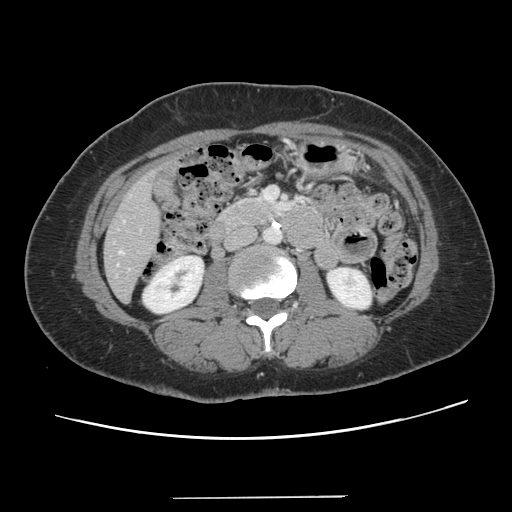
Contrast-enhanced abdominal CT, one axial slice; position 39 of 141 along the scan axis; 120 kVp; intravenous contrast given; soft-tissue window (W 400 / L 40 HU); 2.5 mm slice thickness; 512 × 512 image matrix. Female patient, age 53 years. From the clinical record (not read from this slice): diagnosis: colorectal cancer liver metastases, imaged before liver resection; multiple liver metastases: no; largest metastasis: 14.5 cm; disease in both lobes: yes.
Annotated regions visible in this slice (expert manual segmentation):
- hepatic veins: box from (x=119, y=251) to (x=123, y=254) px
- liver: (x=105, y=171)–(x=159, y=301)
- planned liver remnant (the part of the liver to remain after resection): (x=105, y=215)–(x=159, y=301)